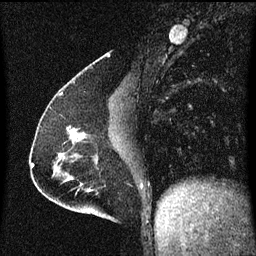
Breast MRI (dynamic contrast-enhanced), one sagittal slice; slice 24 of 60 in the series (ordered by position); dynamic contrast-enhanced series, image 2 of 3 at this slice position (ordered by acquisition); 1.5 T; TE 4.2 ms, TR 8 ms; 2 mm slice thickness; 256 × 256 image matrix, field of view 200 × 200 mm. Female patient, age 51 years.
Annotated regions visible in this slice (semi-automatic segmentation, software-assisted and operator-edited):
- analysis volume of interest (the breast-tissue region the enhancement analysis was run in; not a lesion): bounding box <64,126,91,149> (left, top, right, bottom; pixels)
- tumour enhancement mask (voxels above the 70 % enhancement threshold inside the analysis volume of interest): <68,128,85,143>